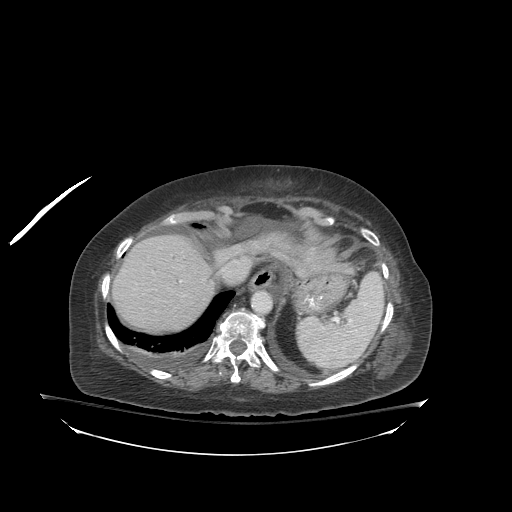
Contrast-enhanced abdominal CT (liver protocol), one axial slice. Position 68 of 81 along the scan axis. Soft-tissue window (W 400 / L 40 HU). 2.5 mm slice thickness. 512 × 512 image matrix, field of view 500 × 500 mm. Case-level facts recorded for this patient, not image findings: diagnosis: hepatocellular carcinoma (patient treated with transarterial chemoembolisation; whether this scan precedes or follows treatment is not stated here); TNM stage (as recorded): Stage-I; Child-Pugh class: B; tumour nodularity: uninodular.
Annotated regions visible in this slice (semi-automatic segmentation, software-assisted and operator-edited):
- abdominal aorta: bounding box [x1, y1, x2, y2] px = [252, 291, 271, 313]
- liver parenchyma outside the tumour (the mass and vessels are separate outlines, so this box may not span the whole liver): [111, 234, 214, 333]